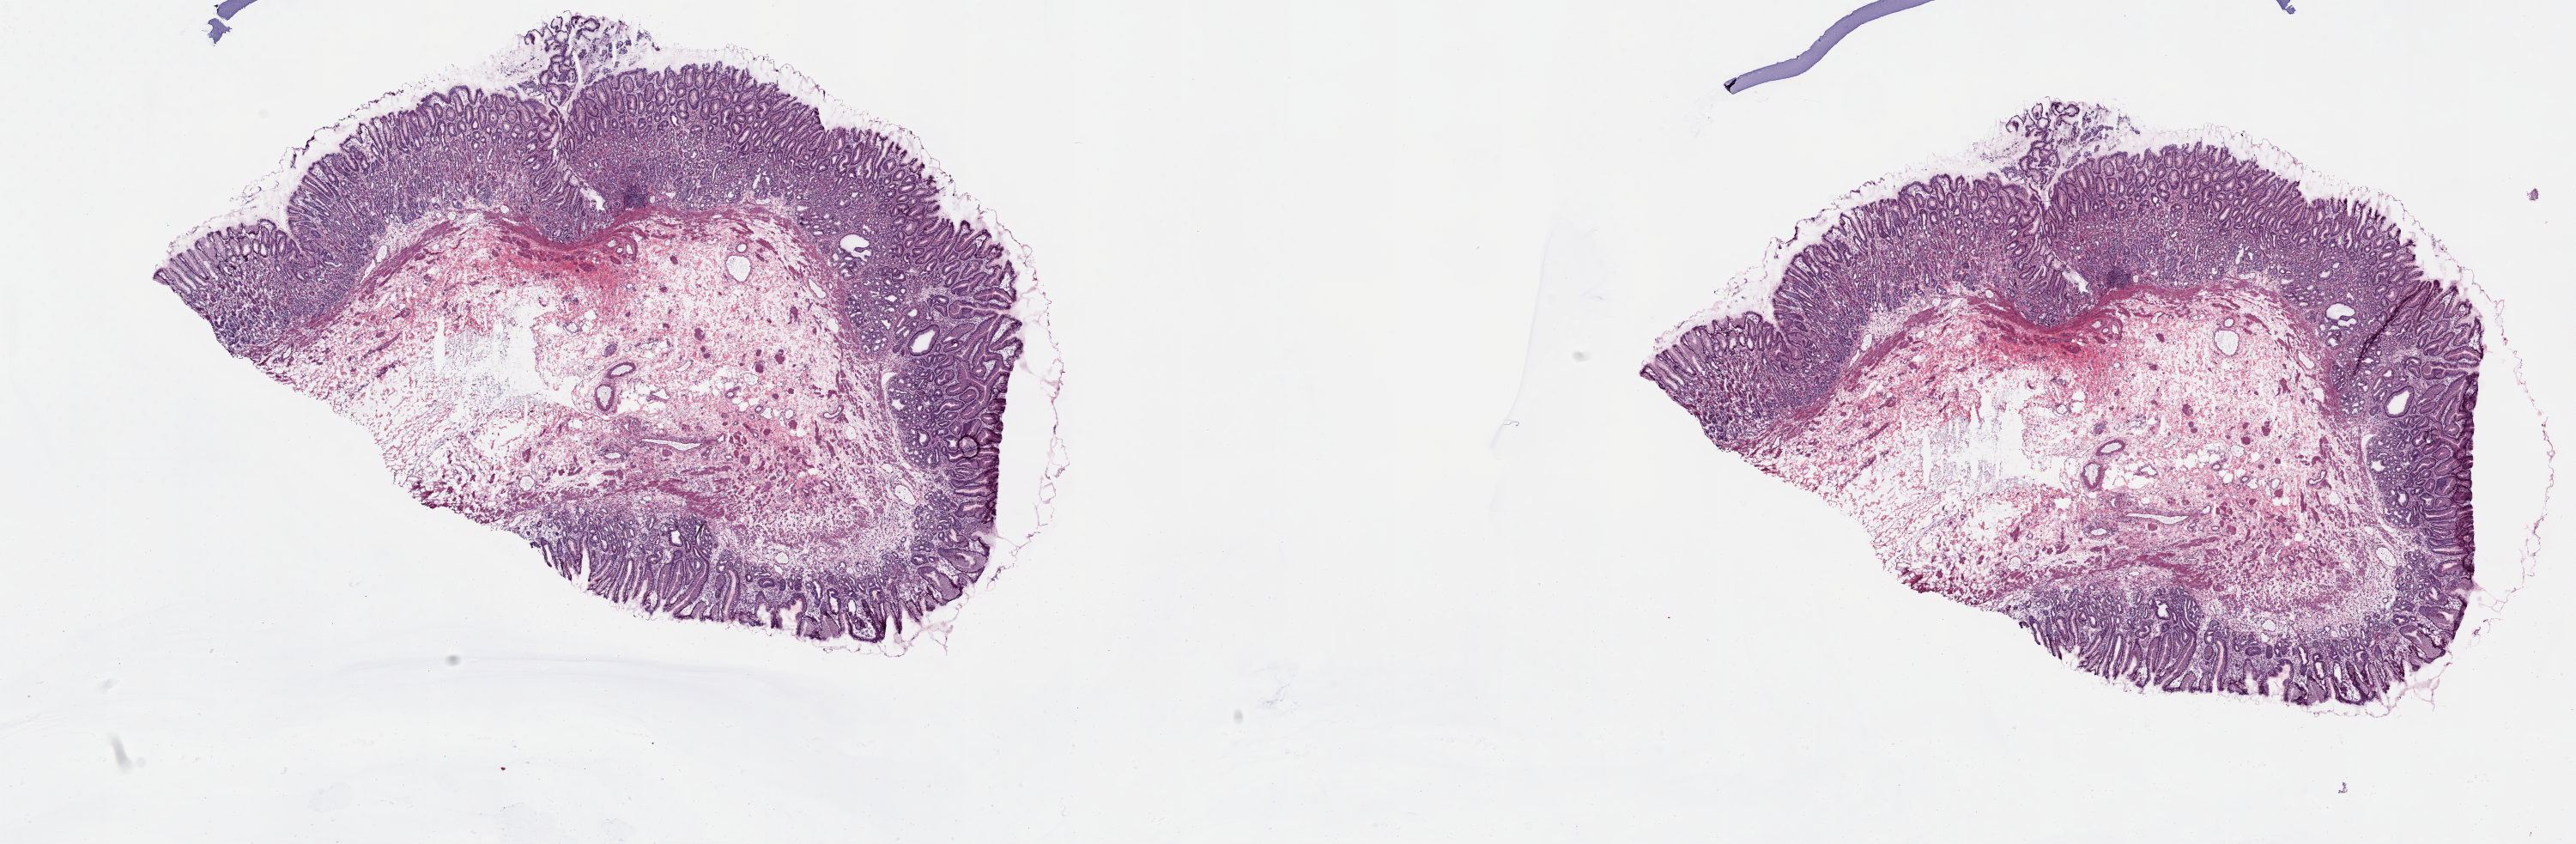
Whole-slide histology image, Hematoxylin and eosin (H&E) stained — whole scanned area (about 23.8 x 7.8 mm) shown as a low-resolution overview. Frozen section. Solid tissue normal (non-tumour tissue) sample from the esophagus. Patient: female, age at initial diagnosis 54 years. Pathologist review of this section (percent, as recorded): tumour cells 0%, tumour nuclei 0%, normal cells 100%, stromal cells 0%, necrosis 0%. Infiltration values recorded for this section: lymphocyte infiltration 3%, monocyte infiltration 0%, neutrophil infiltration 1%.
* this section: solid tissue normal sample (biorepository sample class)
* patient diagnosis: Basaloid squamous cell carcinoma (lower third of esophagus)